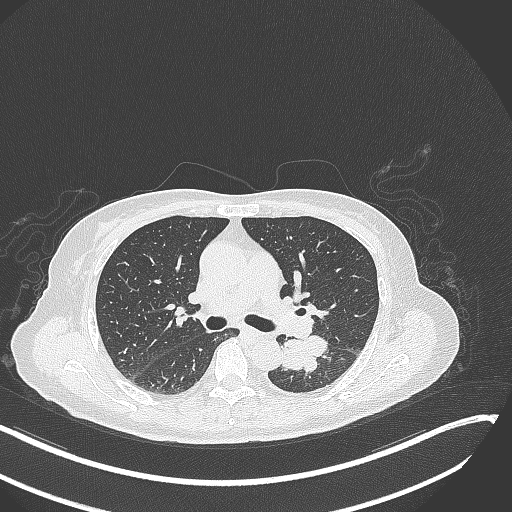
Chest CT, one axial slice. Position 171 of 342 along the scan axis. Reconstruction kernel B70f. 120 kVp. Lung window (W 1500 / L -600 HU). 1 mm slice thickness. 512 × 512 image matrix, field of view 400 × 400 mm. Patient: female, 64 years. Case-level facts recorded for this patient, not image findings: clinical TNM (as recorded): T3 N1 M1; histopathological grade: G3.
Outlined on this slice (bounding box drawn by a radiologist):
- lung tumour (recorded histology: small cell carcinoma): bounding box [x1, y1, x2, y2] px = [280, 332, 331, 379]